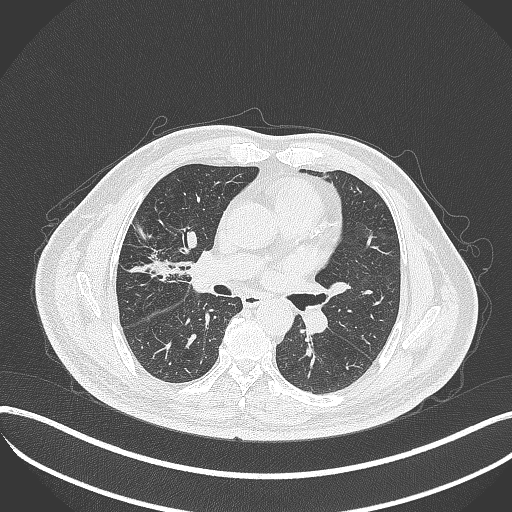
Chest CT, one axial slice. Position 197 of 401 along the scan axis. 120 kVp. Lung window (W 1500 / L -600 HU). 1 mm slice thickness. 512 × 512 image matrix, field of view 400 × 400 mm. Patient: male, 72 years. From the clinical record (not read from this slice): clinical TNM (as recorded): T1c N0 M0; histopathological grade: G2.
Outlined on this slice (rectangle marked by the reading radiologist):
- lung tumour (recorded histology: squamous cell carcinoma): box from (x=183, y=244) to (x=208, y=295) px